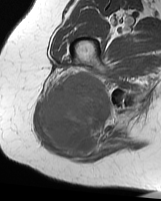
MRI of an extremity soft-tissue mass, one axial slice; position 40 of 70 along the scan axis; MR volume resampled by the dataset authors to the PET/CT grid (not the native acquisition matrix); 3.27 mm slice thickness; 161 × 201 image matrix, field of view 157 × 196 mm. Female patient. From the clinical record (not read from this slice): histological type: synovial sarcoma; grade: intermediate; site of the primary tumour: right buttock.
Outlined on this slice (expert contour drawn on MRI and transferred to this co-registered scan by the dataset authors):
- gross tumour volume including surrounding oedema: box from (x=42, y=70) to (x=112, y=158) px
- gross tumour volume (mass): (x=42, y=70)–(x=112, y=151)